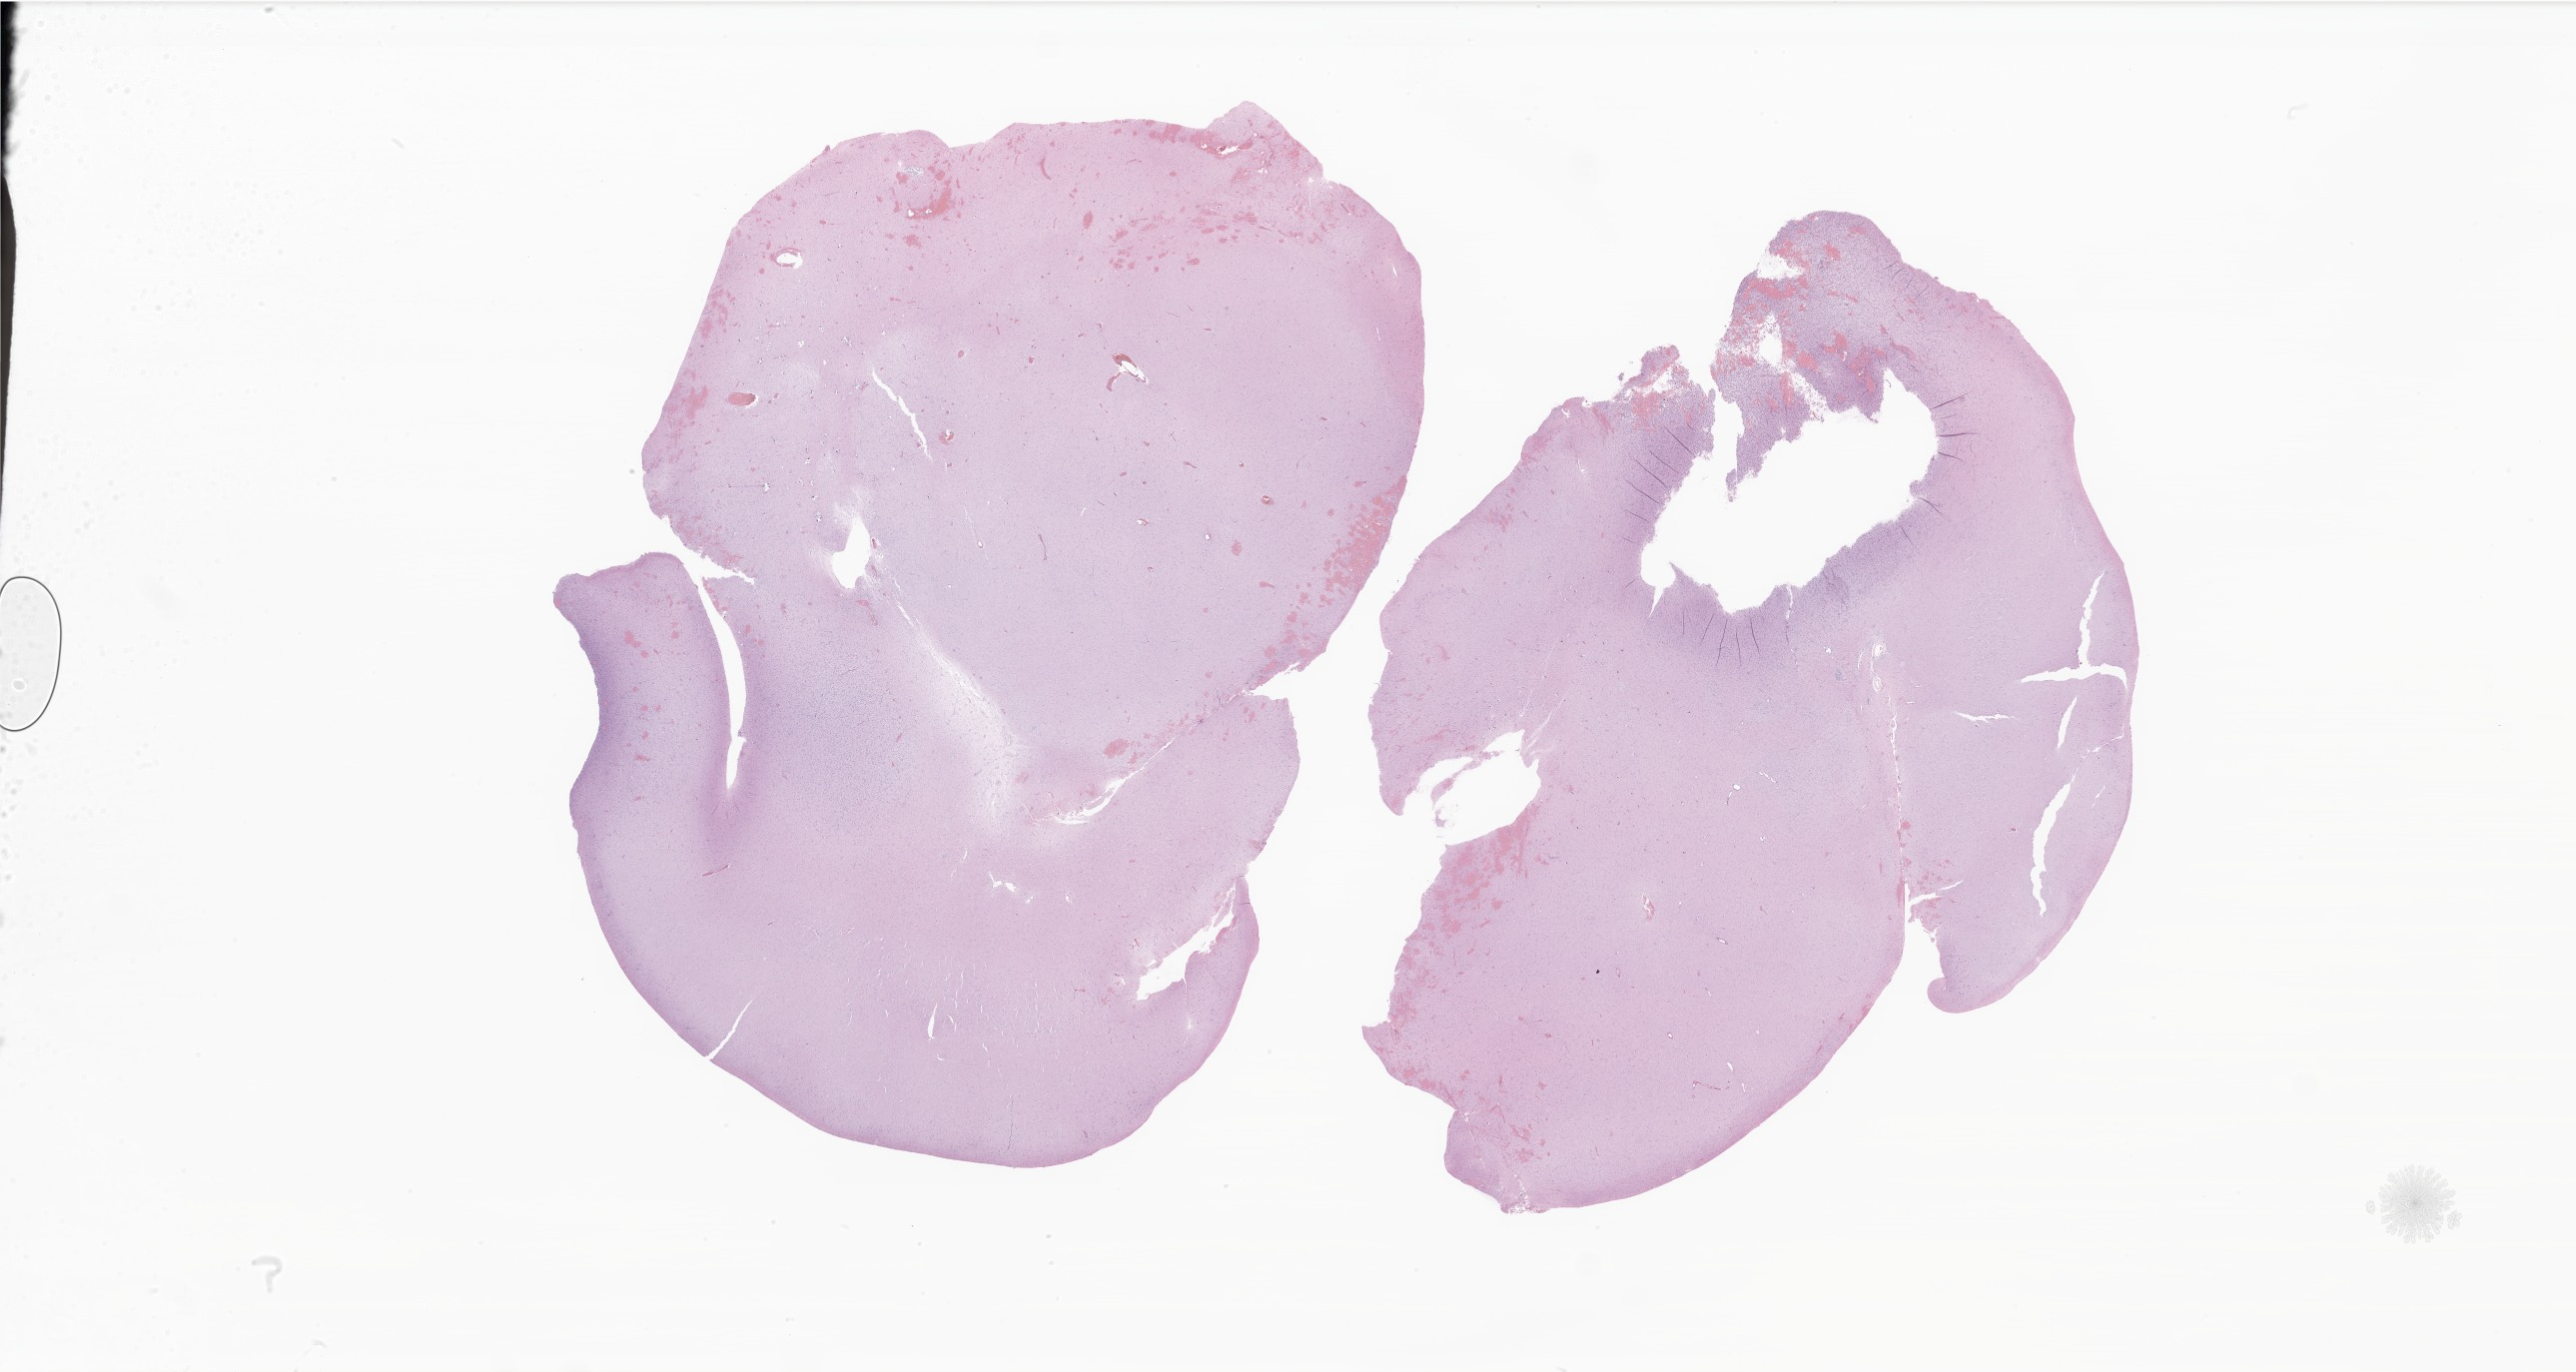
H&E whole-slide image of tumor tissue from the brain — a low-resolution overview of the entire scanned area, about 43.5 x 23.2 mm. Formalin-fixed paraffin-embedded section. Patient male; age 231 months (19 years 3 months).
• recorded diagnosis: Ganglioglioma, NOS